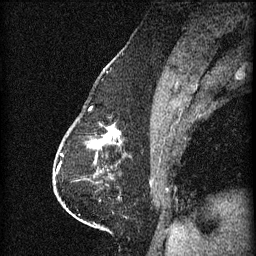
Breast MRI (dynamic contrast-enhanced), one sagittal slice. Position 26 of 60 along the scan axis. 3 images stored at this slice position (order not interpretable as contrast timing). 1.5 T. TE 4.2 ms, TR 11 ms. 256 × 256 image matrix, field of view 180 × 180 mm. Patient: female, 63 years.
Outlined on this slice (semi-automatically segmented with operator editing):
- analysis volume of interest (the breast-tissue region the enhancement analysis was run in; not a lesion): bounding box [x1, y1, x2, y2] px = [88, 124, 123, 153]
- tumour enhancement mask (voxels above the 70 % enhancement threshold inside the analysis volume of interest): [92, 128, 121, 149]